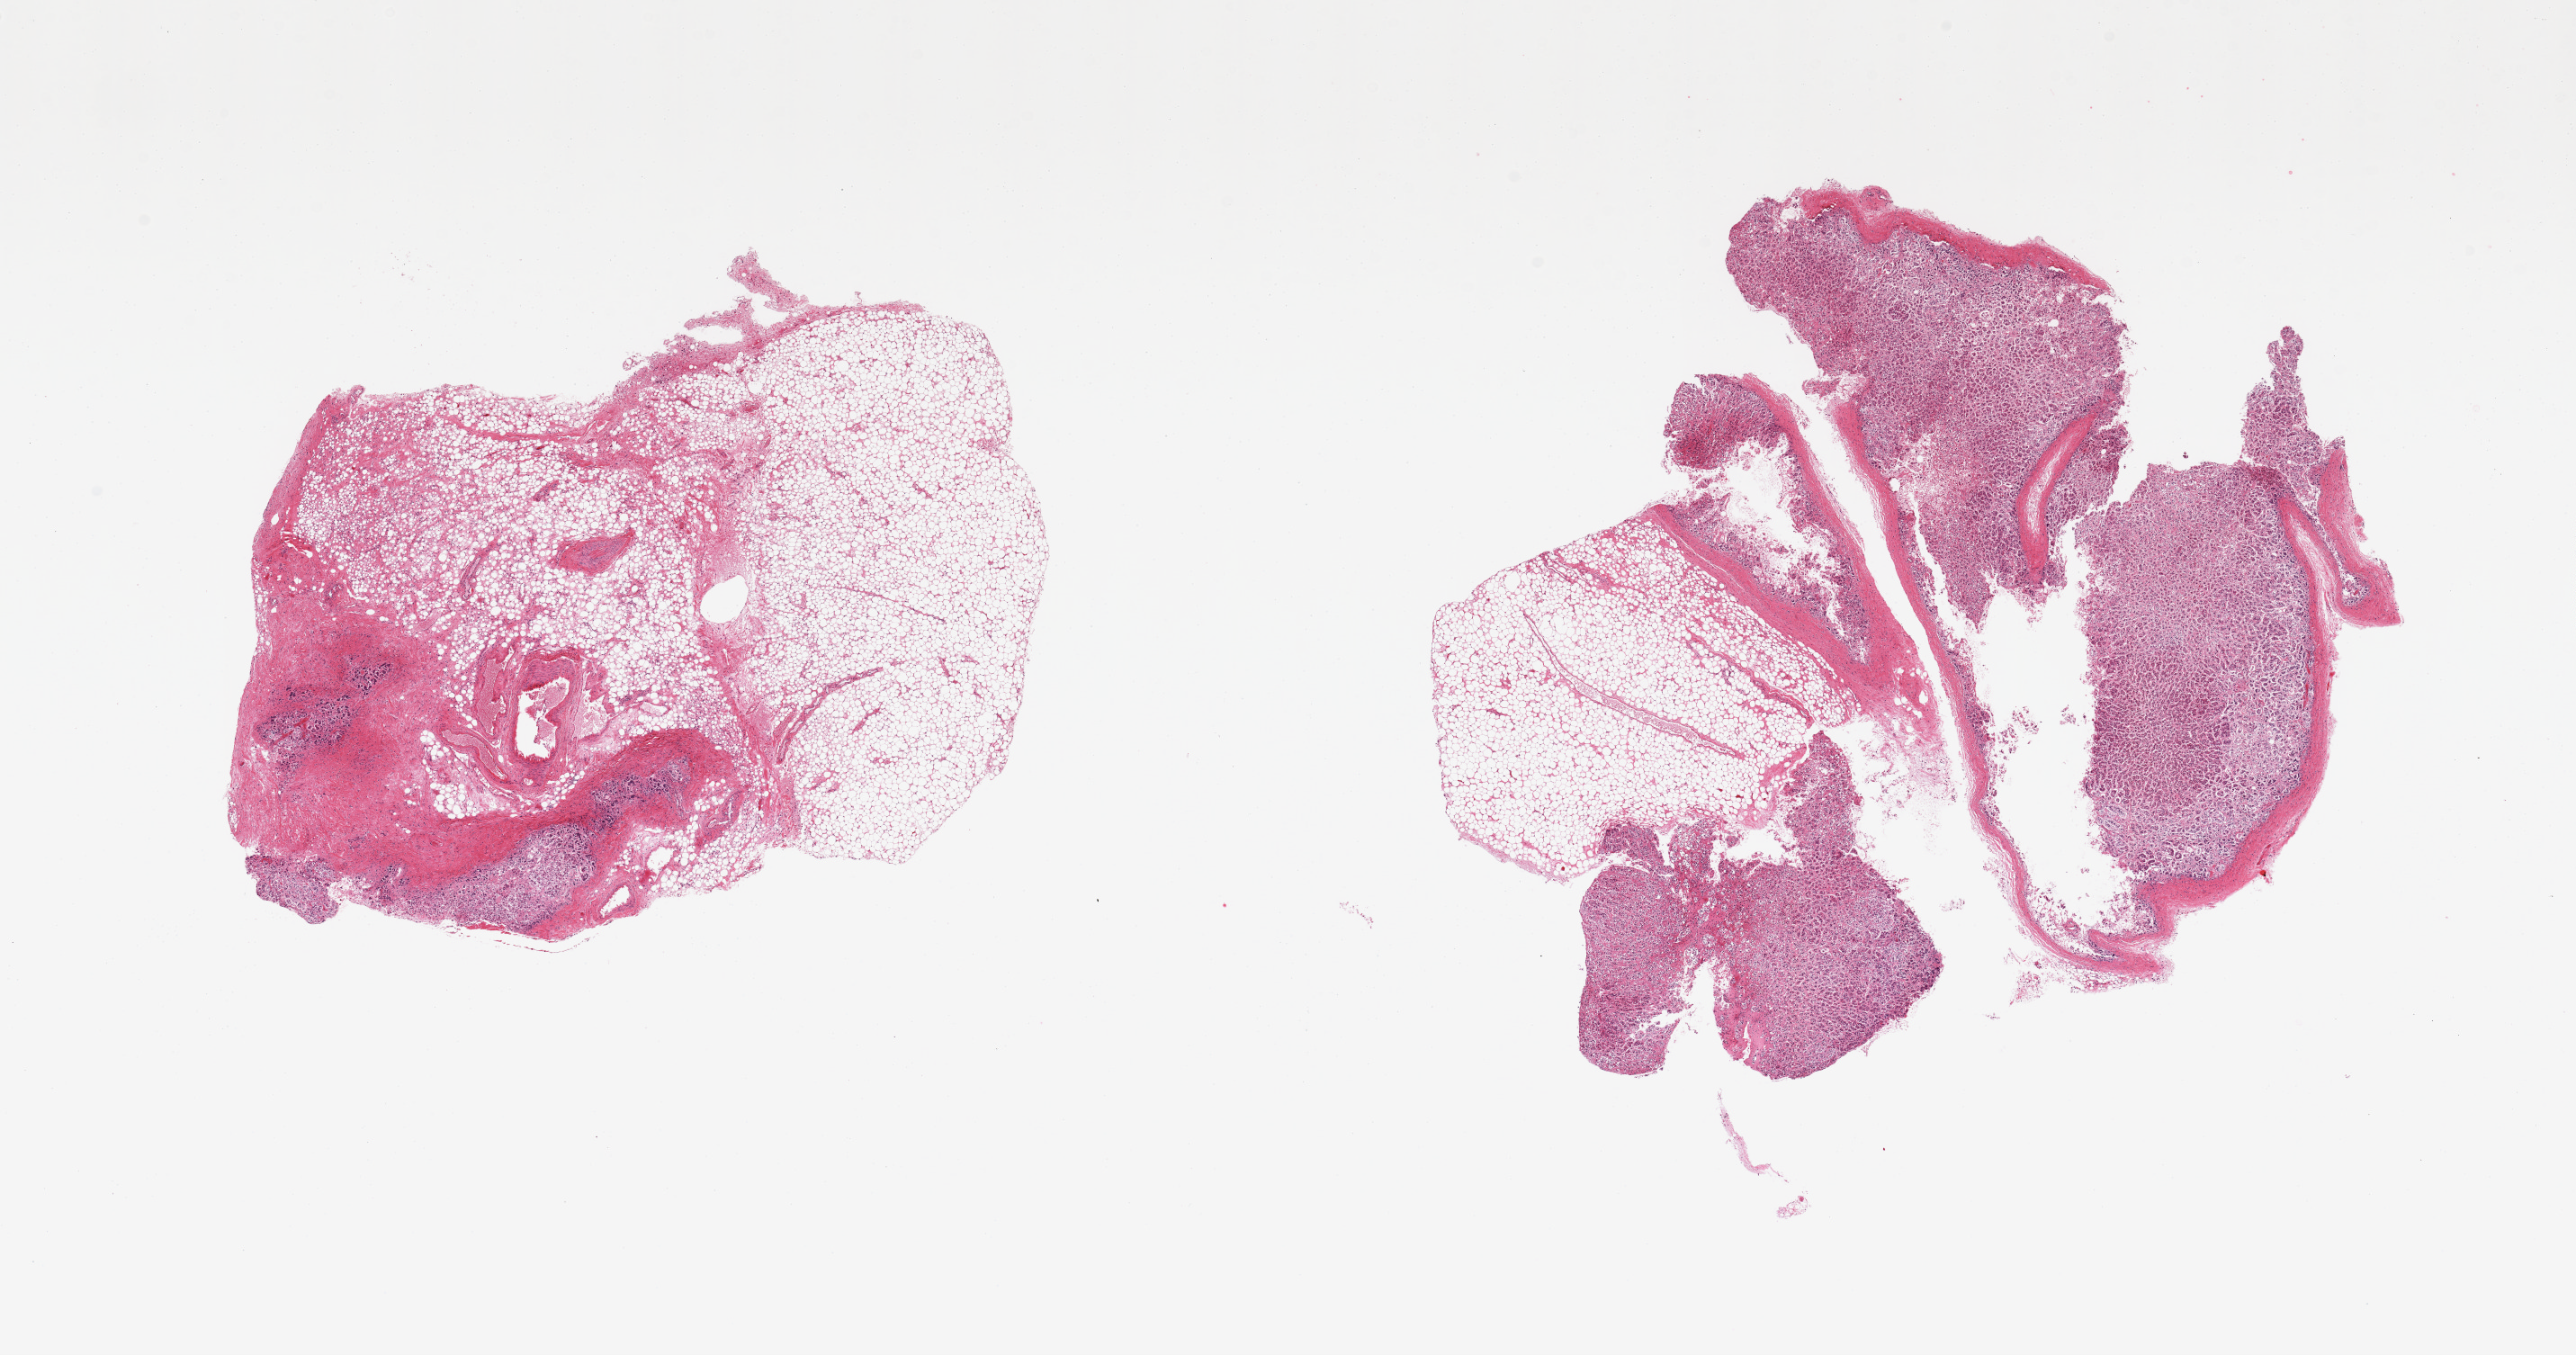
Haematoxylin and eosin whole-slide image — a low-resolution overview of the entire scanned area, about 22.6 x 11.9 mm (from a 20x scan); PAXgene-fixed, paraffin-embedded tissue; target tissue: adrenal gland; tissue donor sample. Male donor.
Reviewer comment on this tissue sample: 2 pieces; some areas have moderate autolysis; 1 piece has 90% fat content, other has 40%.